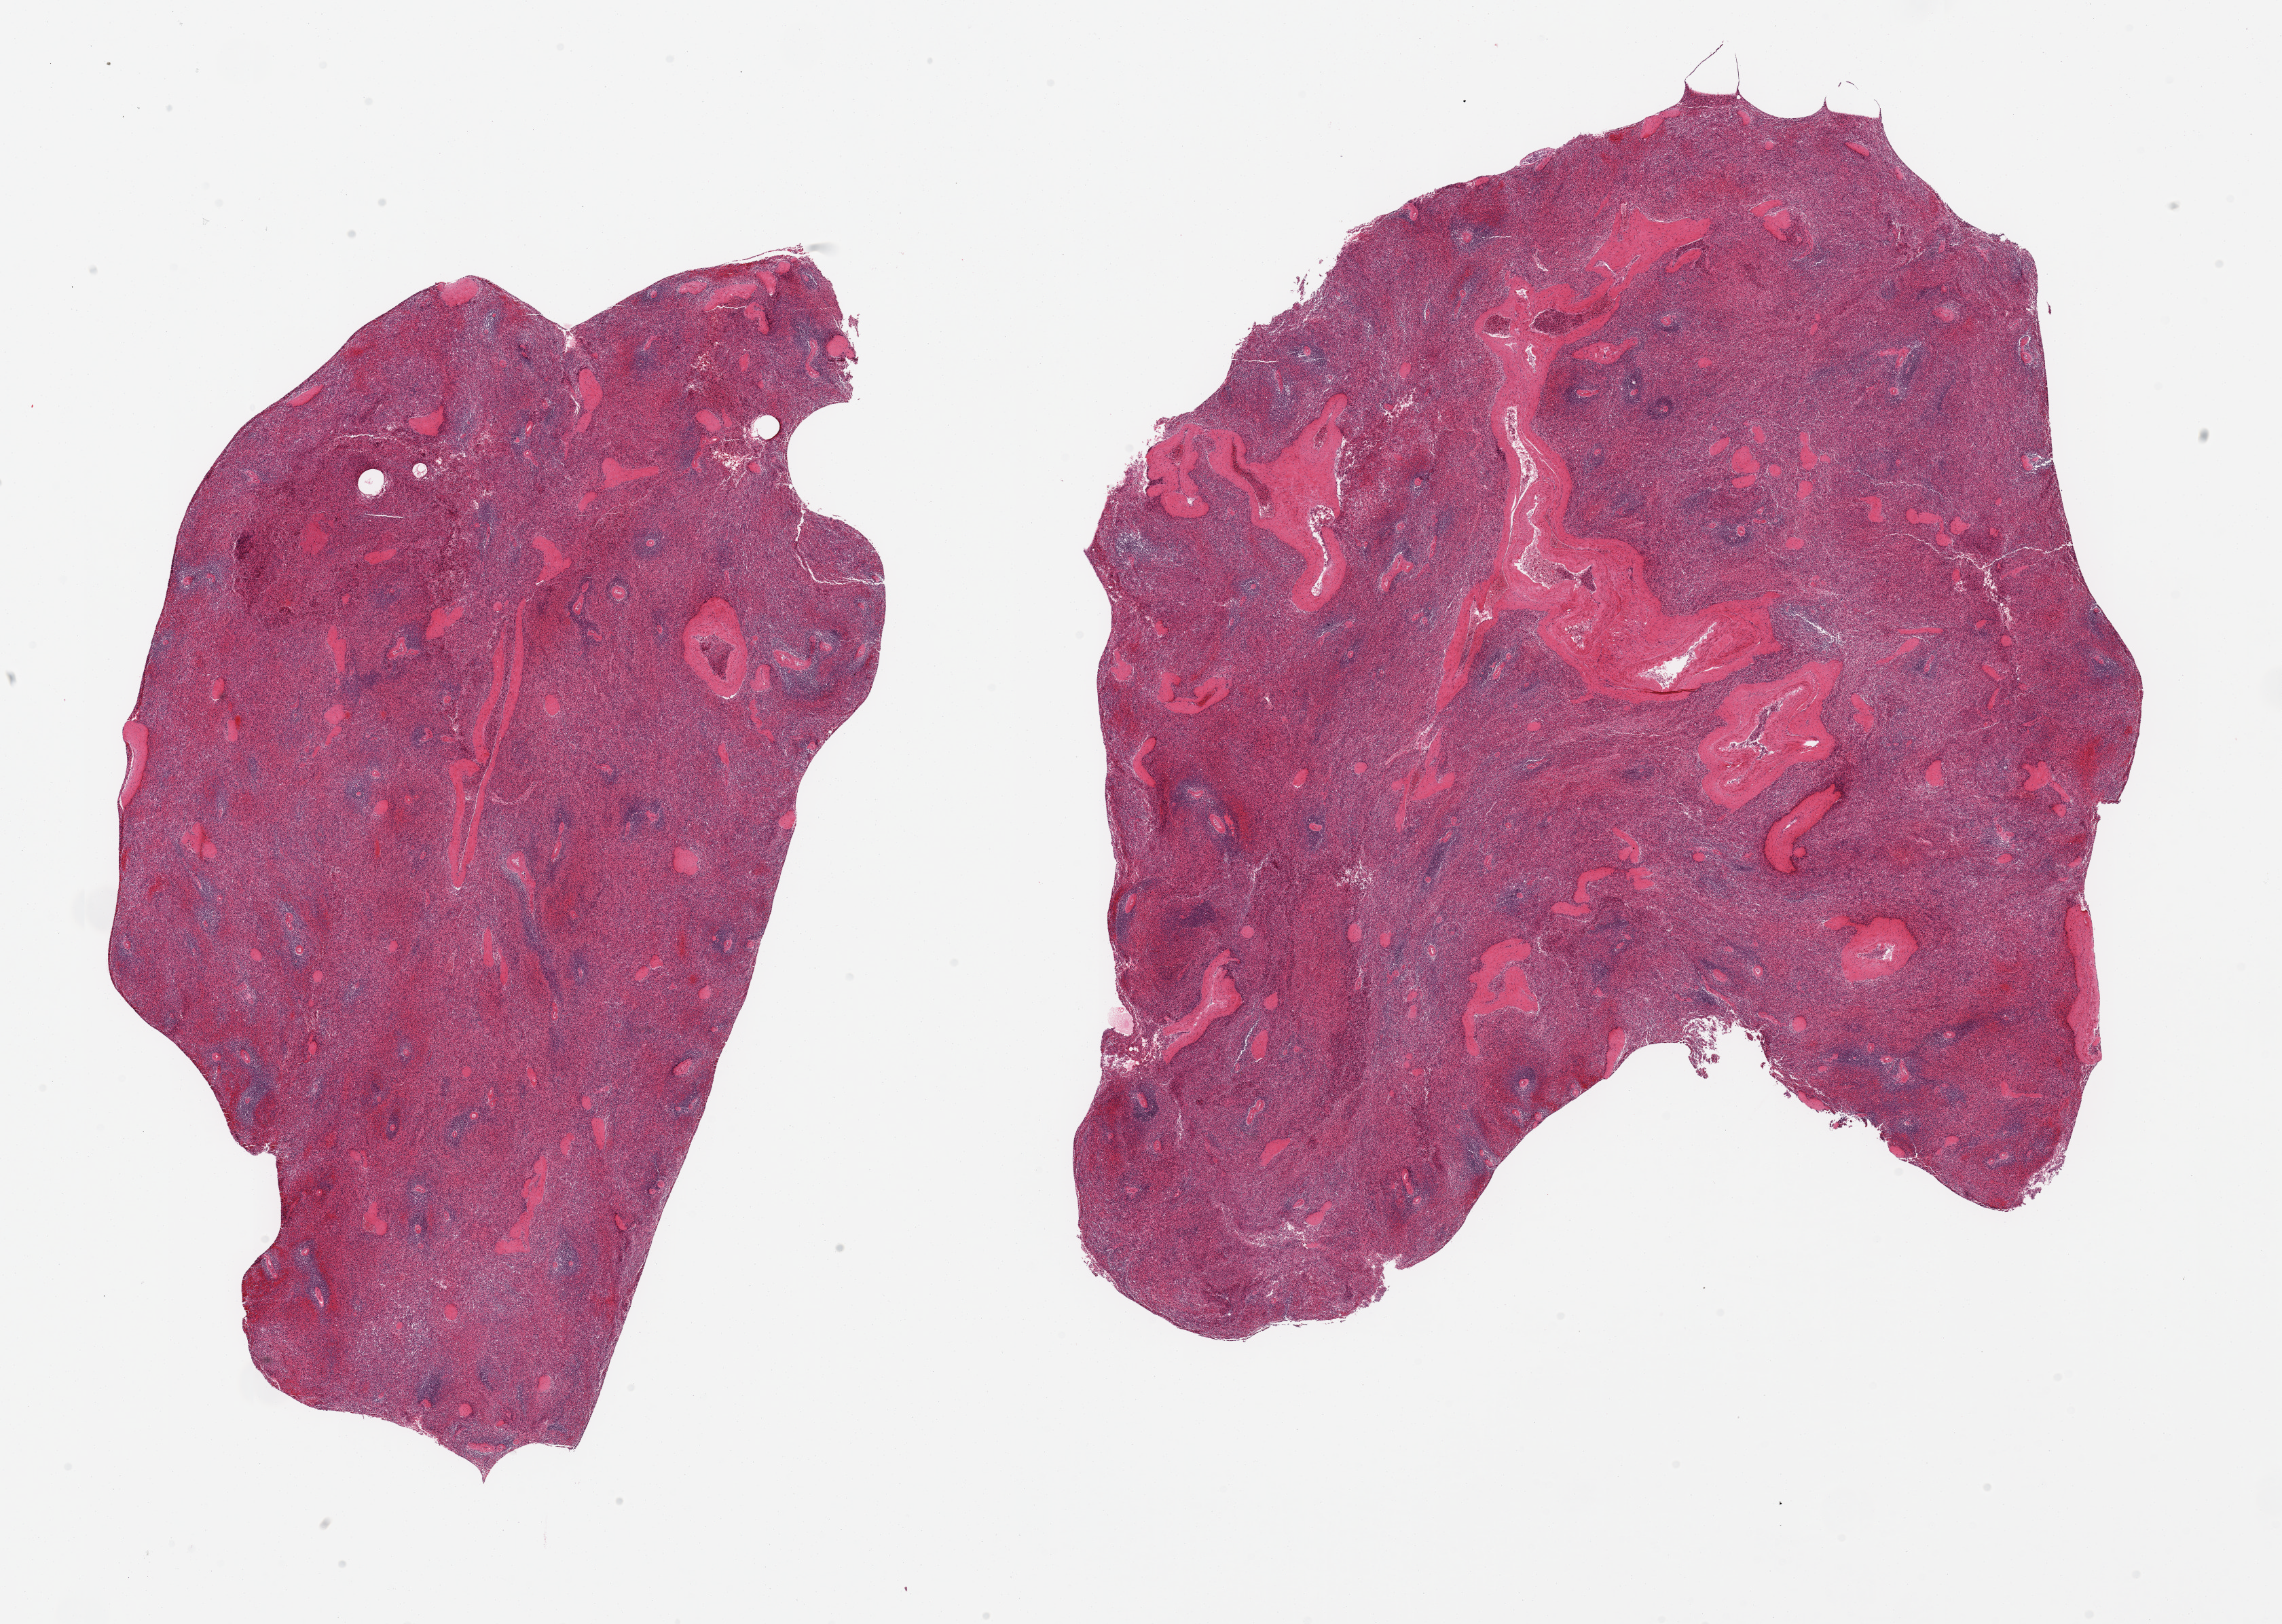
Haematoxylin and eosin whole-slide image, a low-resolution overview of the entire scanned area, about 26.6 x 18.9 mm, PAXgene-fixed, paraffin-embedded tissue, sampled site (target tissue): spleen, donor tissue sample.
Pathologist's review note for this sample: 2 piecesno abnormalities.